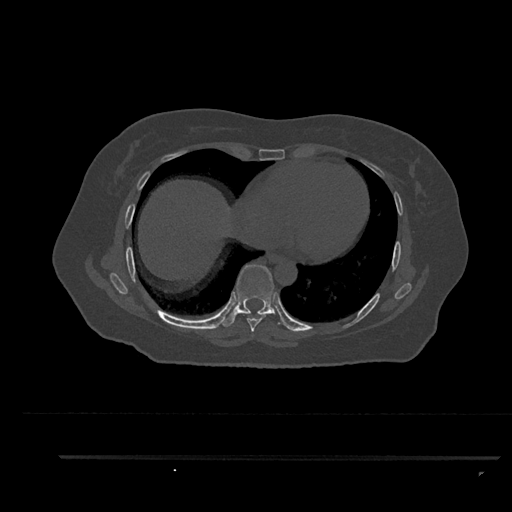
CT including the spine, one axial slice; slice 481 of 797 in the series (ordered by position); reconstruction kernel Br40s/3; bone window (W 1800 / L 400 HU); 0.5 mm slice thickness; 512 × 512 image matrix, field of view 408 × 408 mm. Female patient, age 44 years. Case-level facts recorded for this patient, not image findings: primary cancer: renal; vertebrae with lytic lesions (as recorded): L1.
Structures marked on this image (semi-automatically segmented with operator editing):
- T7 vertebra: bounding box <242,313,266,332> (left, top, right, bottom; pixels)
- T8 vertebra: <222,264,285,327>